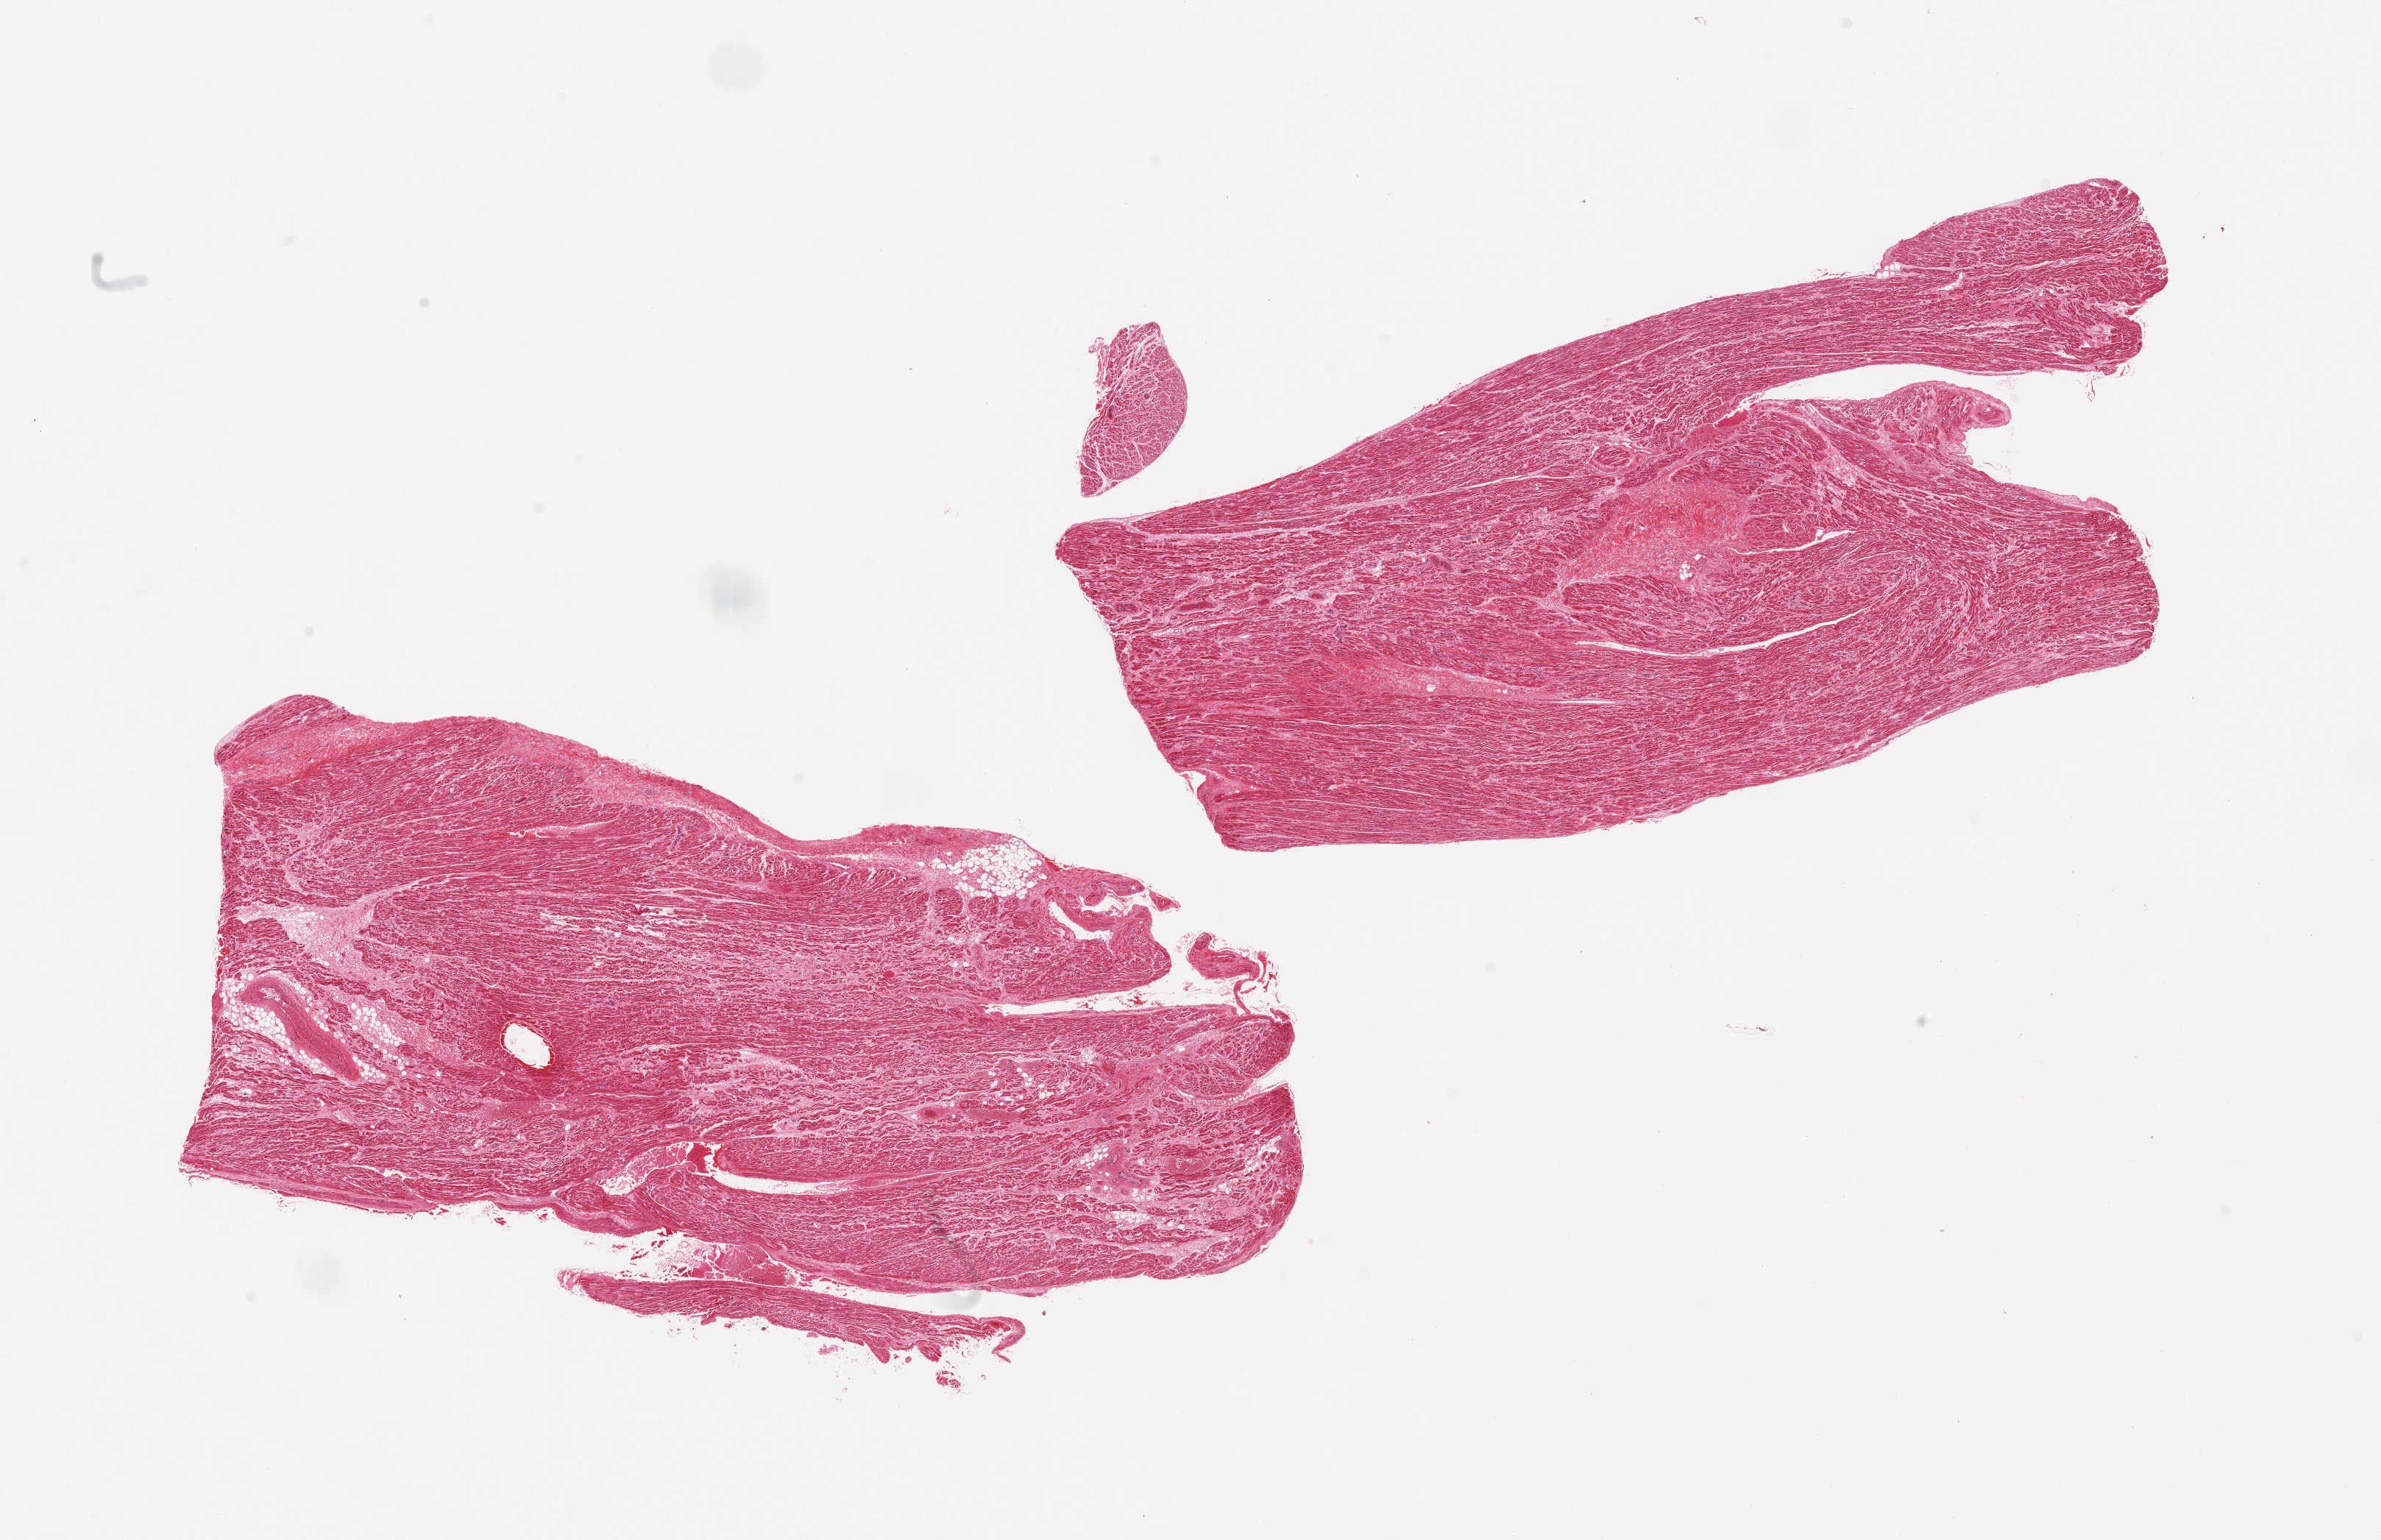
Digitized H&E-stained section, shown as a low-resolution overview of the whole scanned area (about 25.6 x 16.6 mm, from a 20x scan), PAXgene-fixed paraffin-embedded (PFPE) section, section of auricular appendage (target tissue), donor tissue sample.
Reviewer comment on this tissue sample: 2 pieces; well dissected; minimal fat.